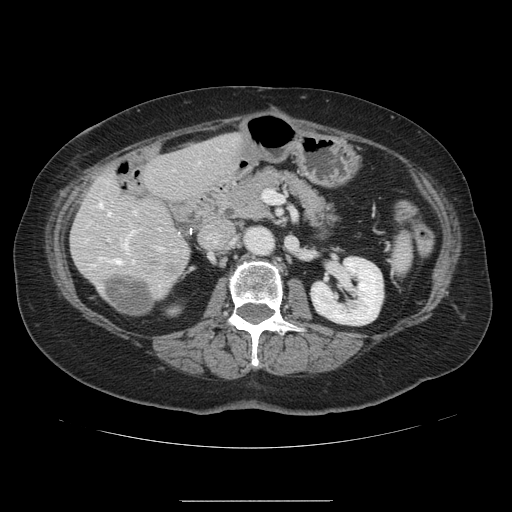
Contrast-enhanced abdominal CT, one axial slice; position 53 of 141 along the scan axis; 120 kVp; intravenous contrast given; soft-tissue window (W 400 / L 40 HU); 2.5 mm slice thickness; 512 × 512 image matrix. Female patient, age 74 years. From the clinical record (not read from this slice): diagnosis: colorectal cancer liver metastases, imaged before liver resection; multiple liver metastases: yes; largest metastasis: 7 cm.
Annotated regions visible in this slice (expert manual segmentation):
- hepatic veins: bounding box (x1, y1, x2, y2) in pixels: (99, 203, 134, 264)
- liver: (72, 134, 242, 316)
- planned liver remnant (the part of the liver to remain after resection): (118, 134, 242, 315)
- portal vein (with intrahepatic branches): (107, 211, 162, 250)
- liver metastasis: (109, 280, 155, 314)
- liver metastasis: (150, 259, 186, 288)